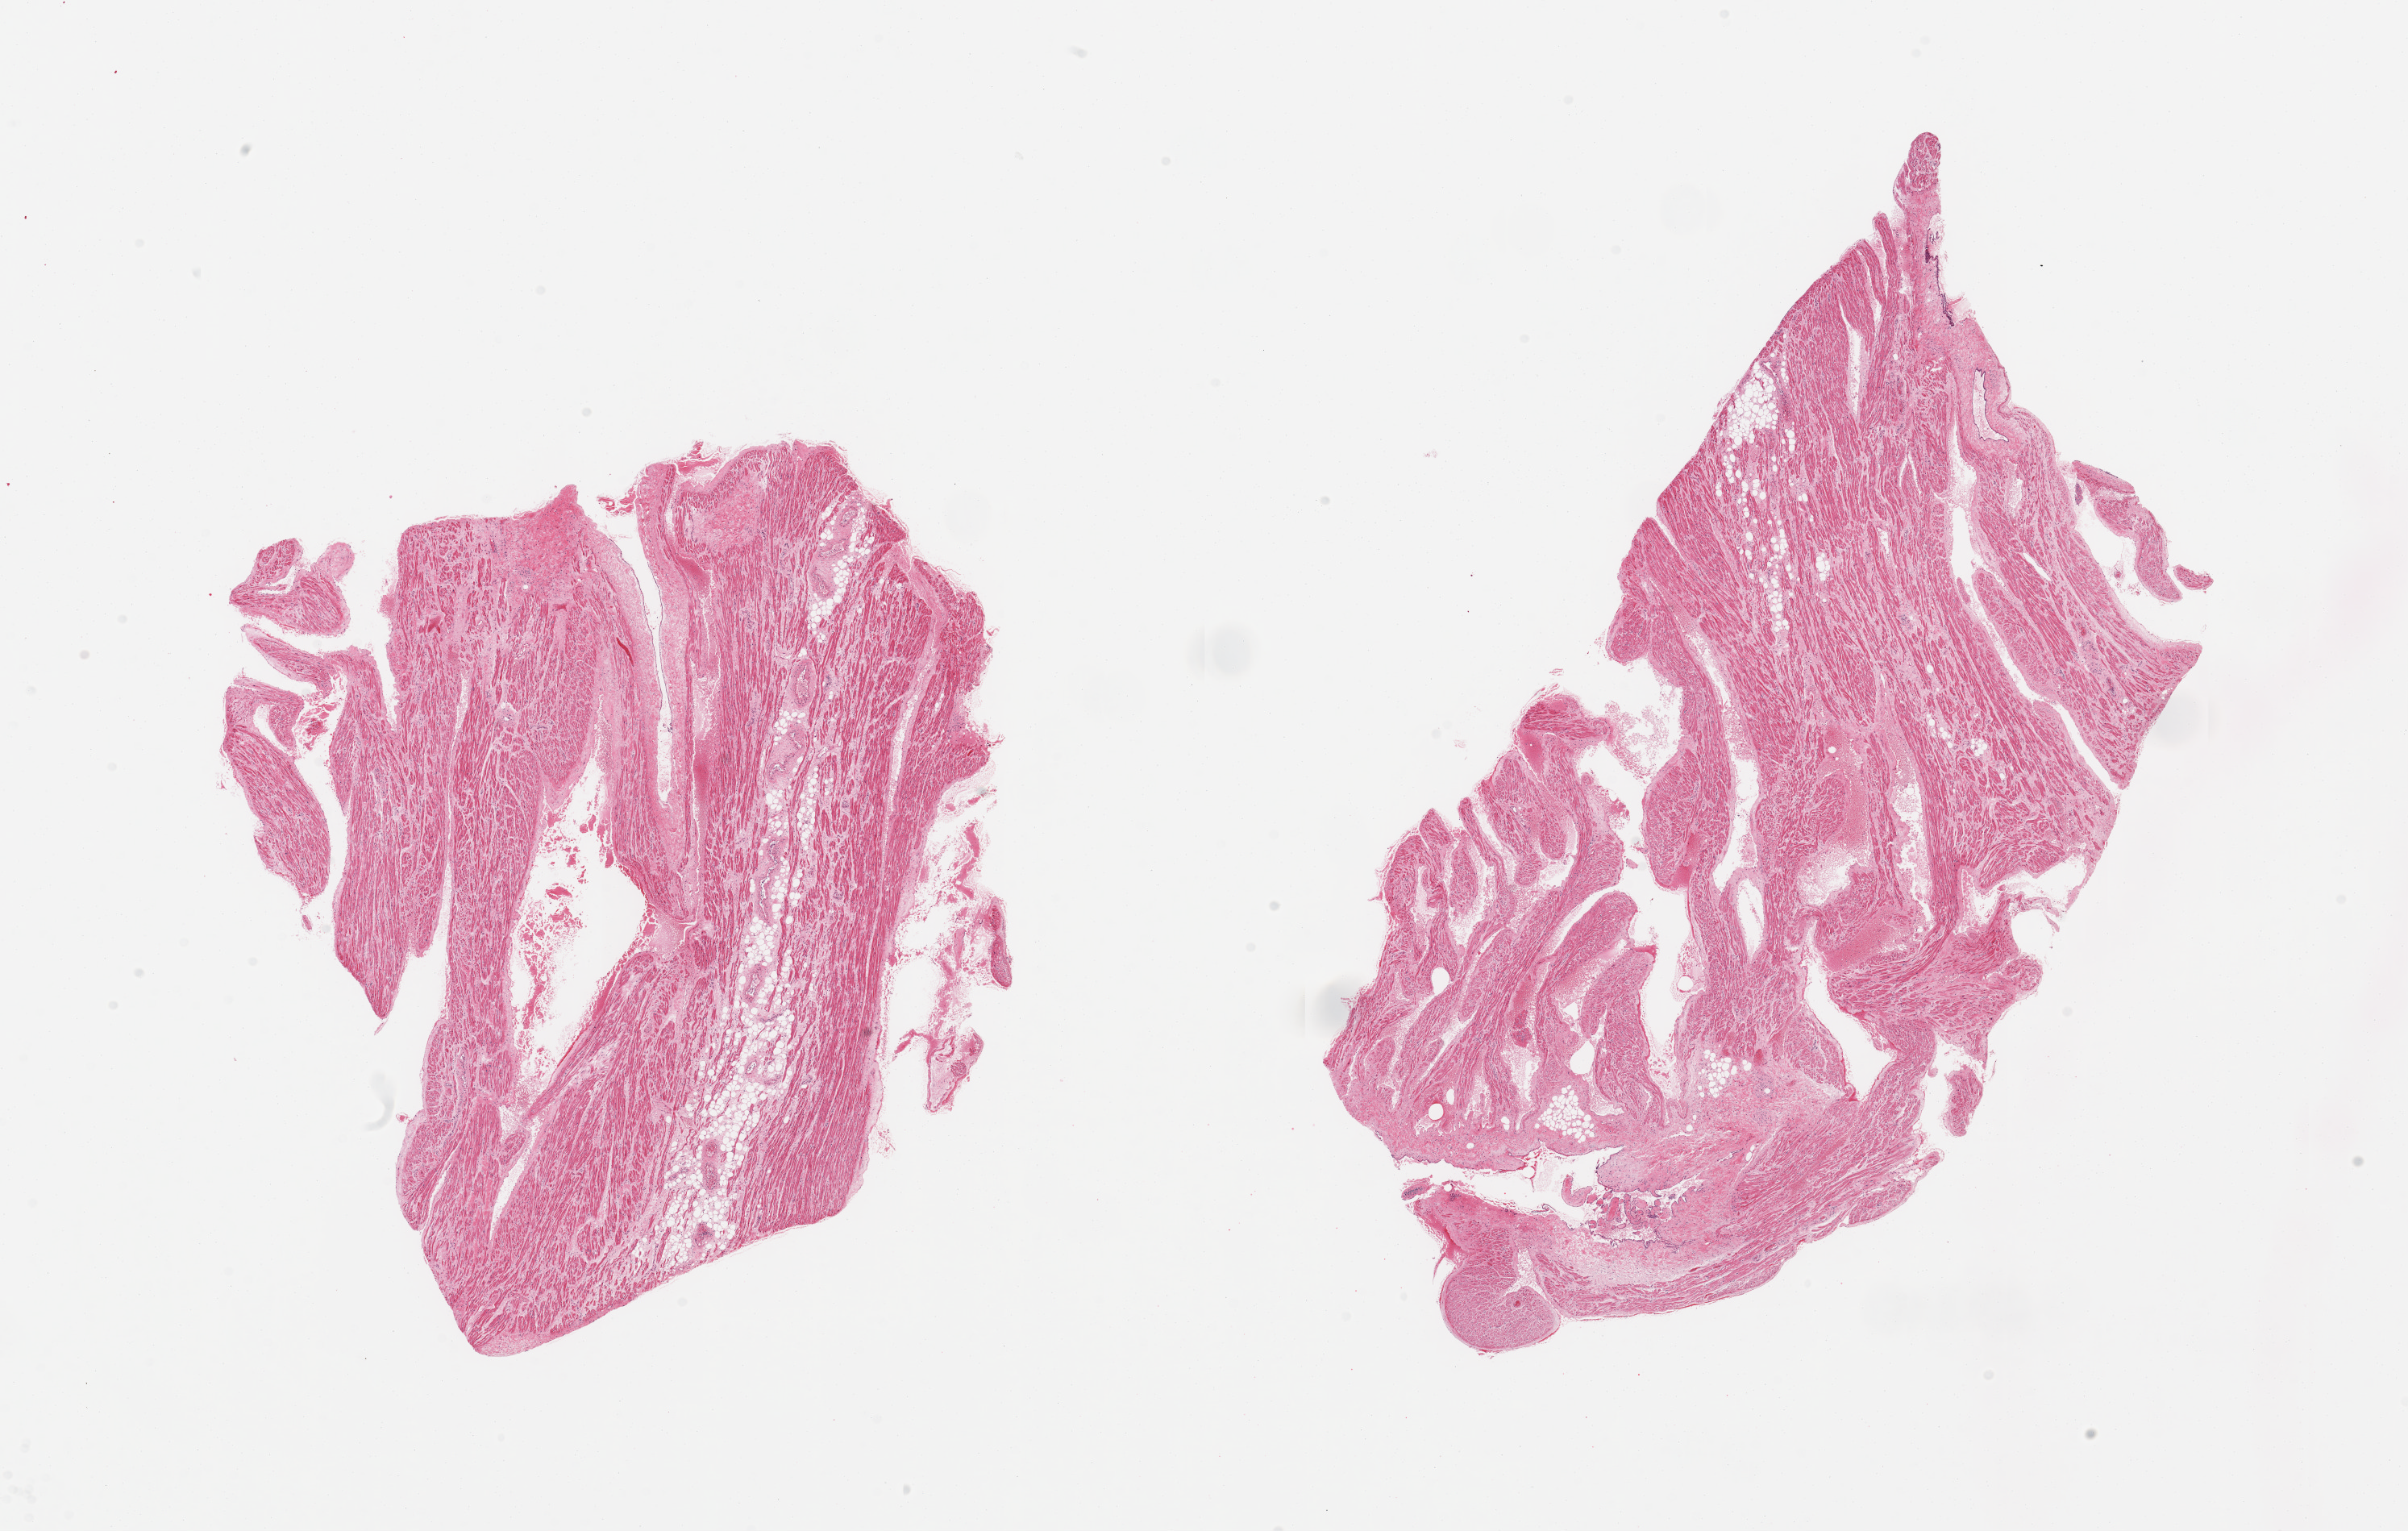
Digitized H&E-stained section, whole scanned area (about 23.6 x 15.0 mm, slide scanned at 20x) shown as a low-resolution overview; PAXgene-fixed, paraffin-embedded tissue; section of auricular appendage (target tissue); donor tissue sample. Donor: male.
Pathologist's review note for this sample: 2 pieces, no abnormalities.